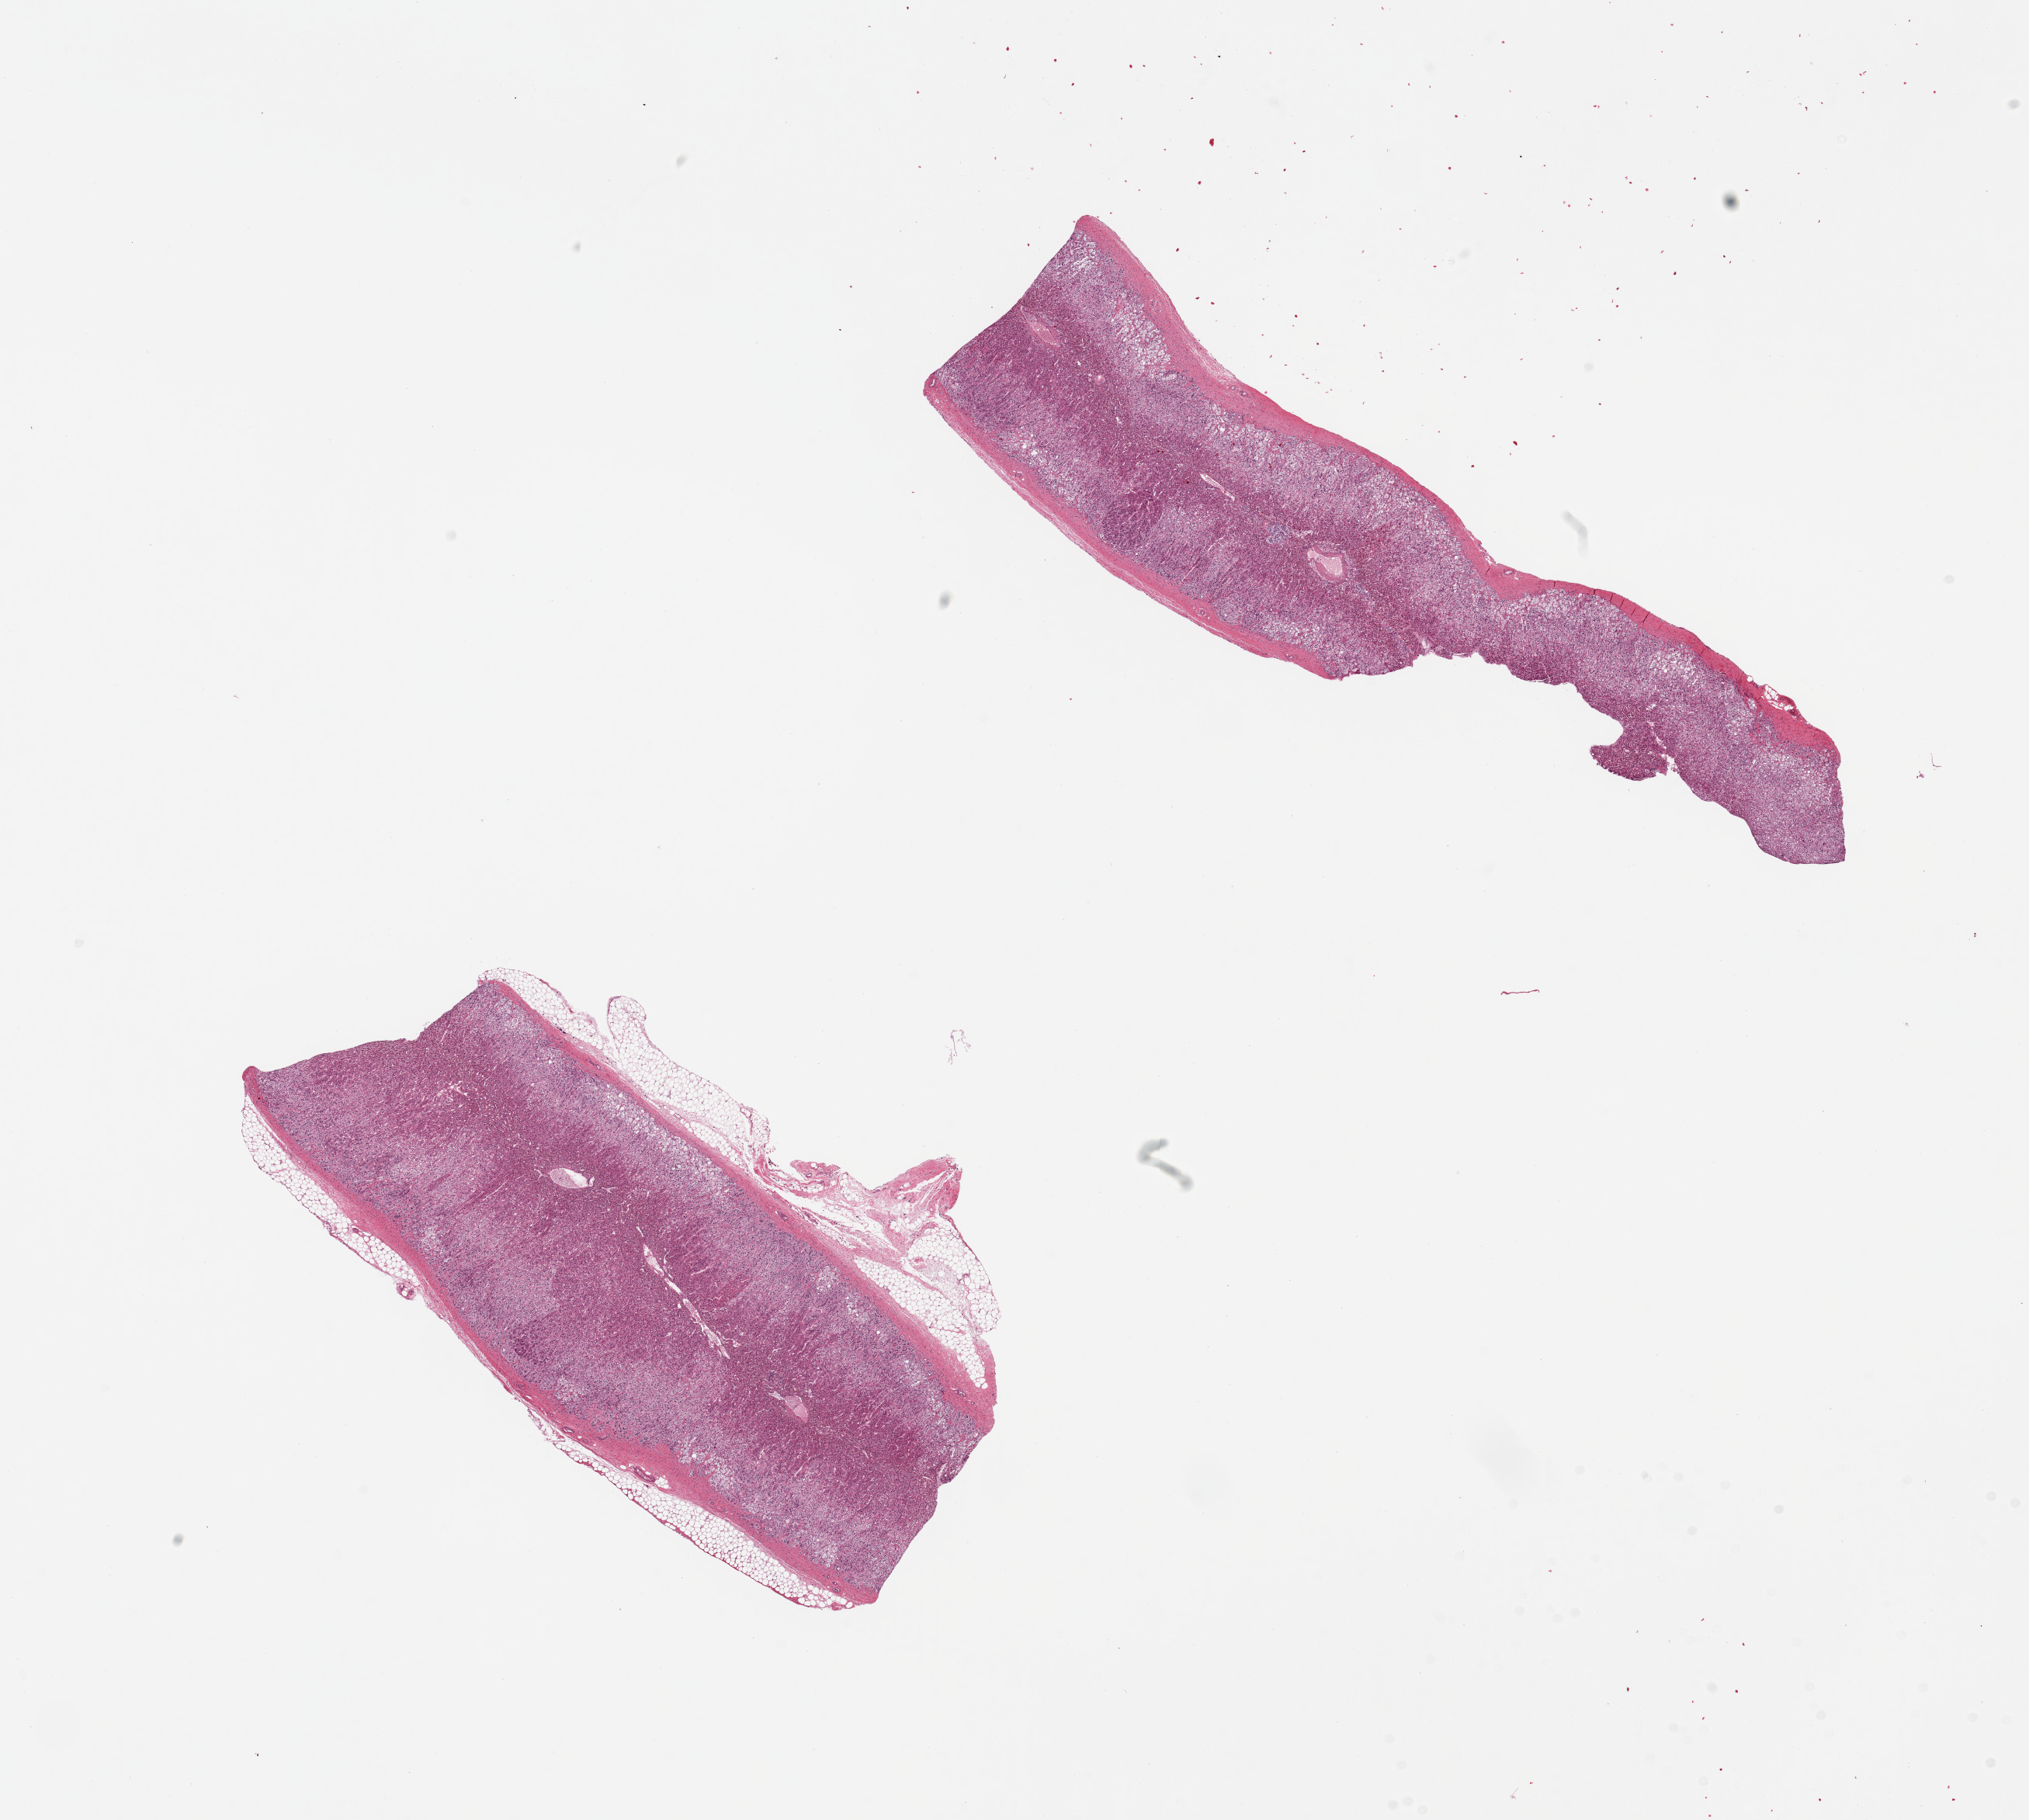
Digitized H&E-stained section, a low-resolution overview of the entire scanned area, about 20.7 x 18.5 mm. PAXgene-fixed, paraffin-embedded tissue. Sampled site (target tissue): adrenal gland. Donor tissue sample. Donor sex: male.
* pathologist's review note for this sample: 2 pieces, all cortex, ~1-1.5mm rim of adherent fat on one aliquot